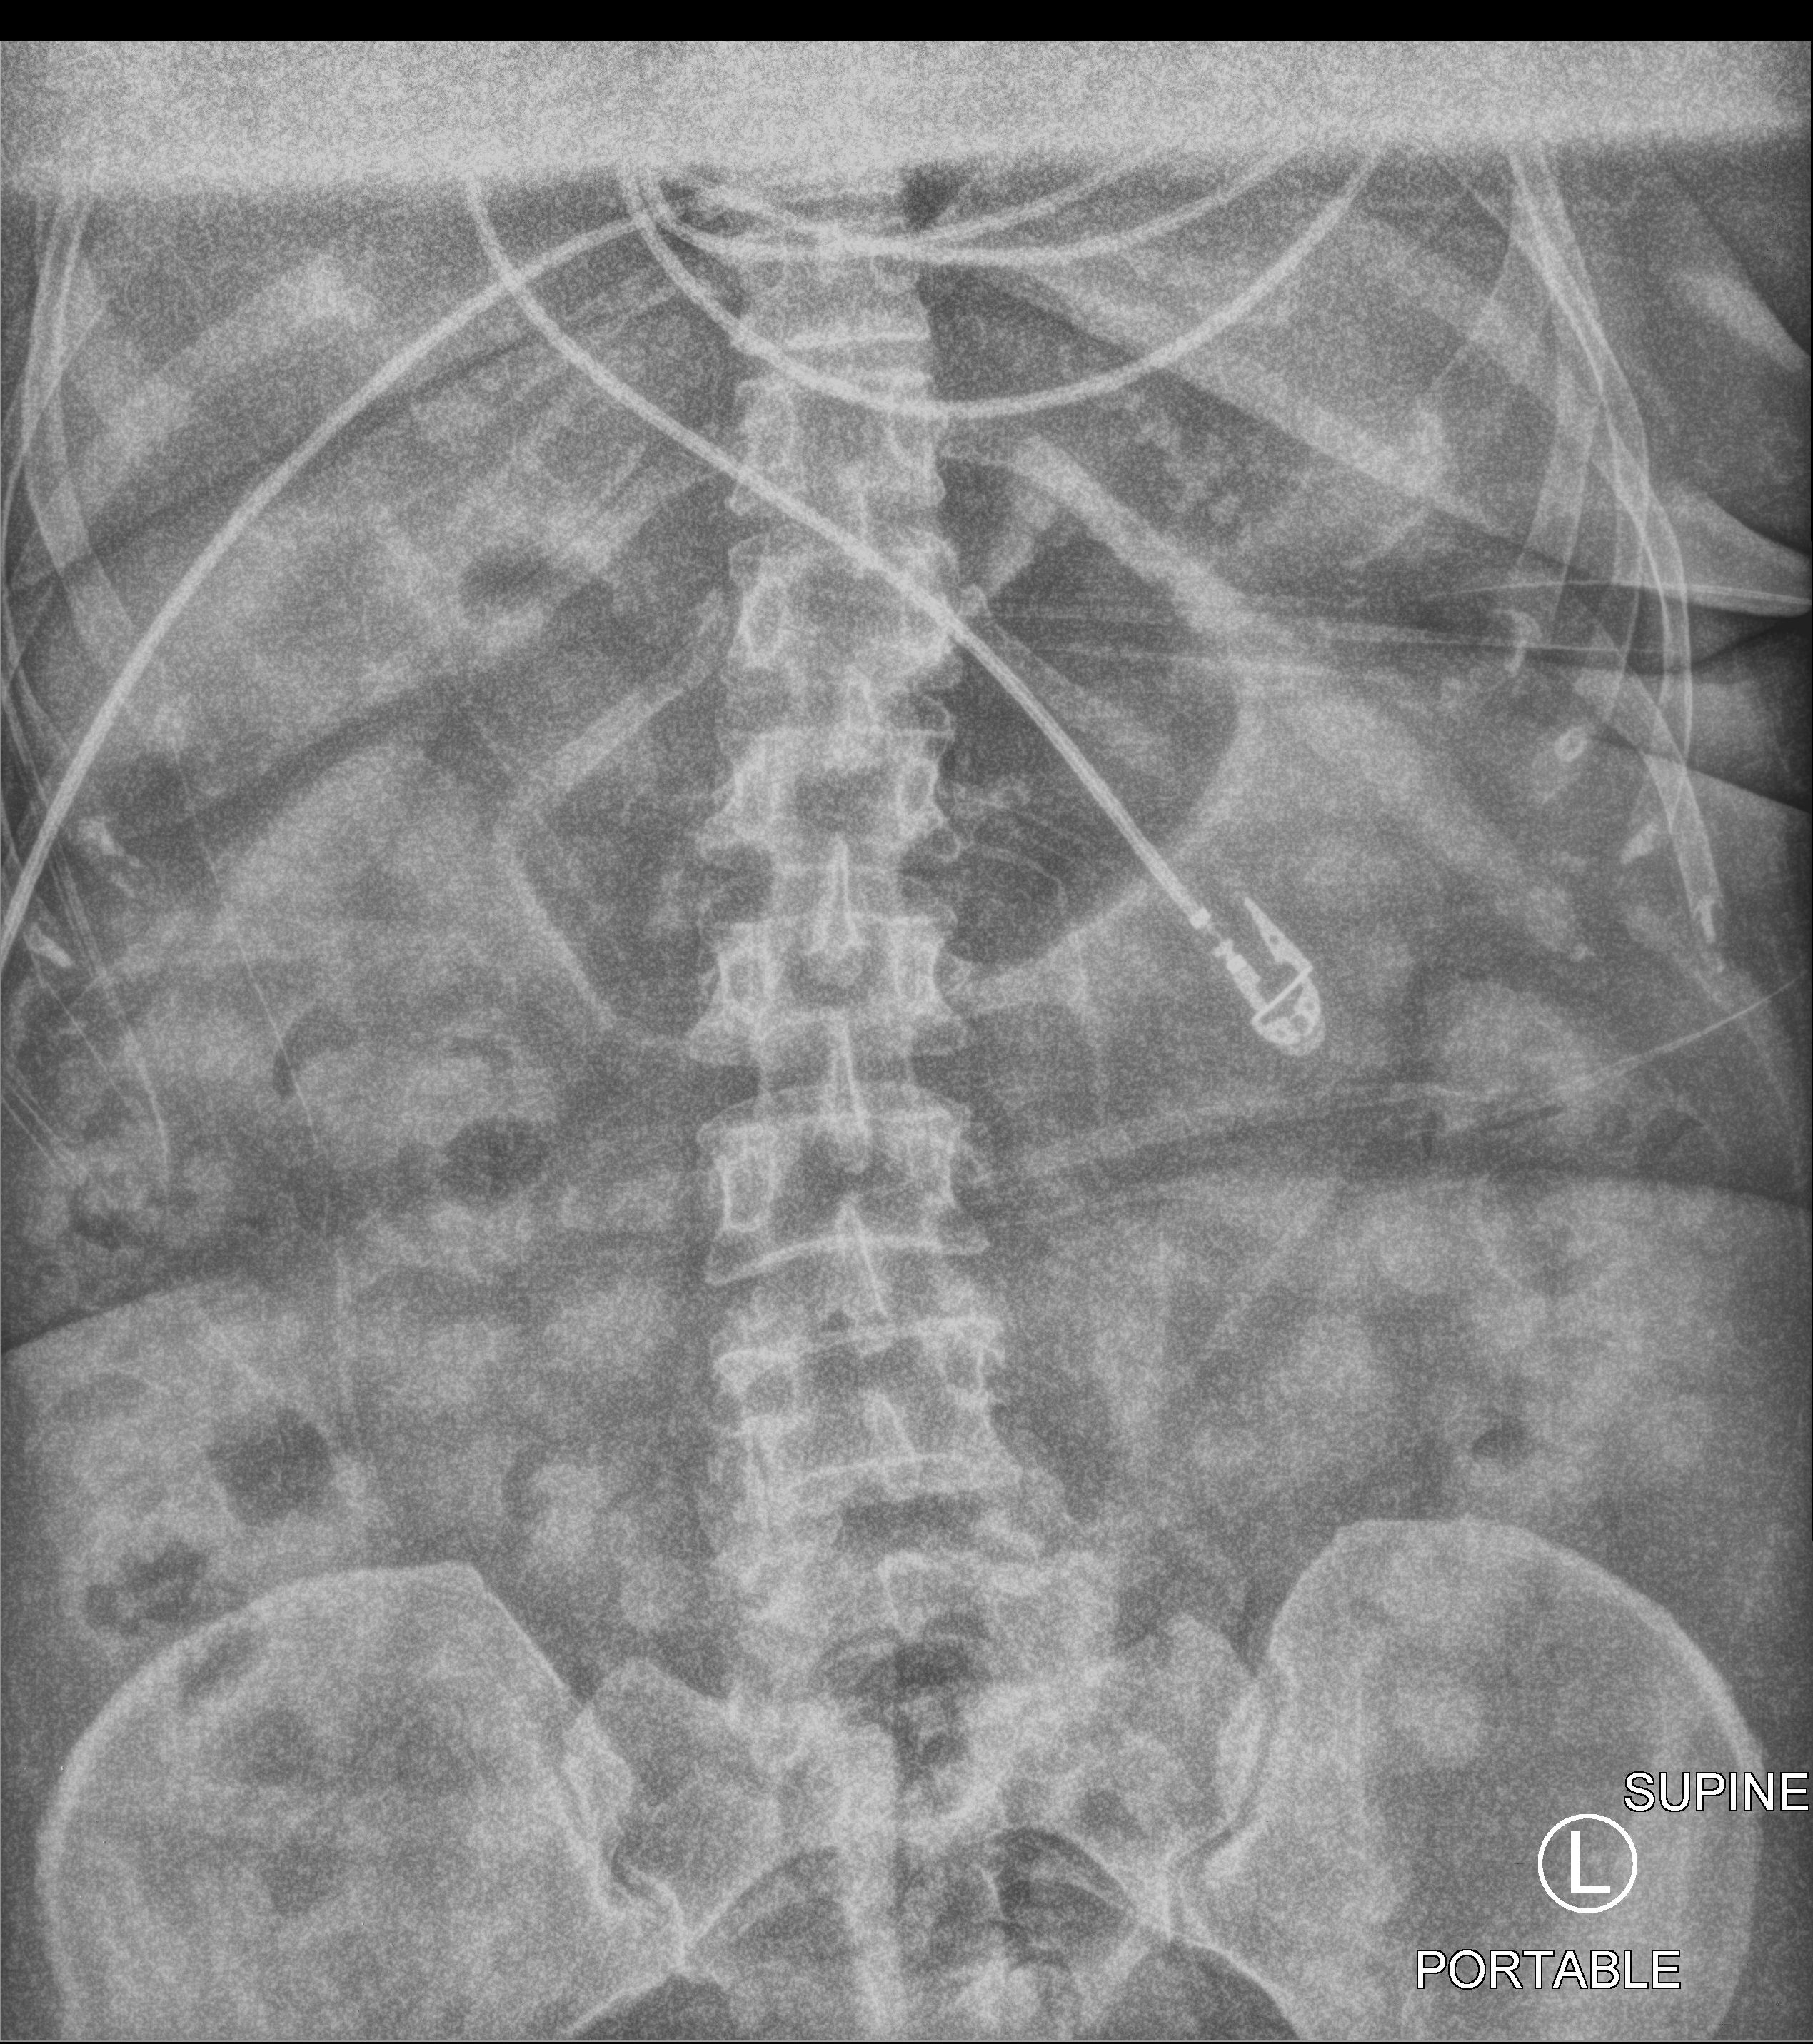
Portable abdomen radiograph. Female patient hospitalised with COVID-19, age 60–74 years.
From the hospital-stay record, not from the radiograph (when in the stay this image was taken is not recorded): mechanically ventilated during this hospital stay: yes; admitted to intensive care during this hospital stay: yes.